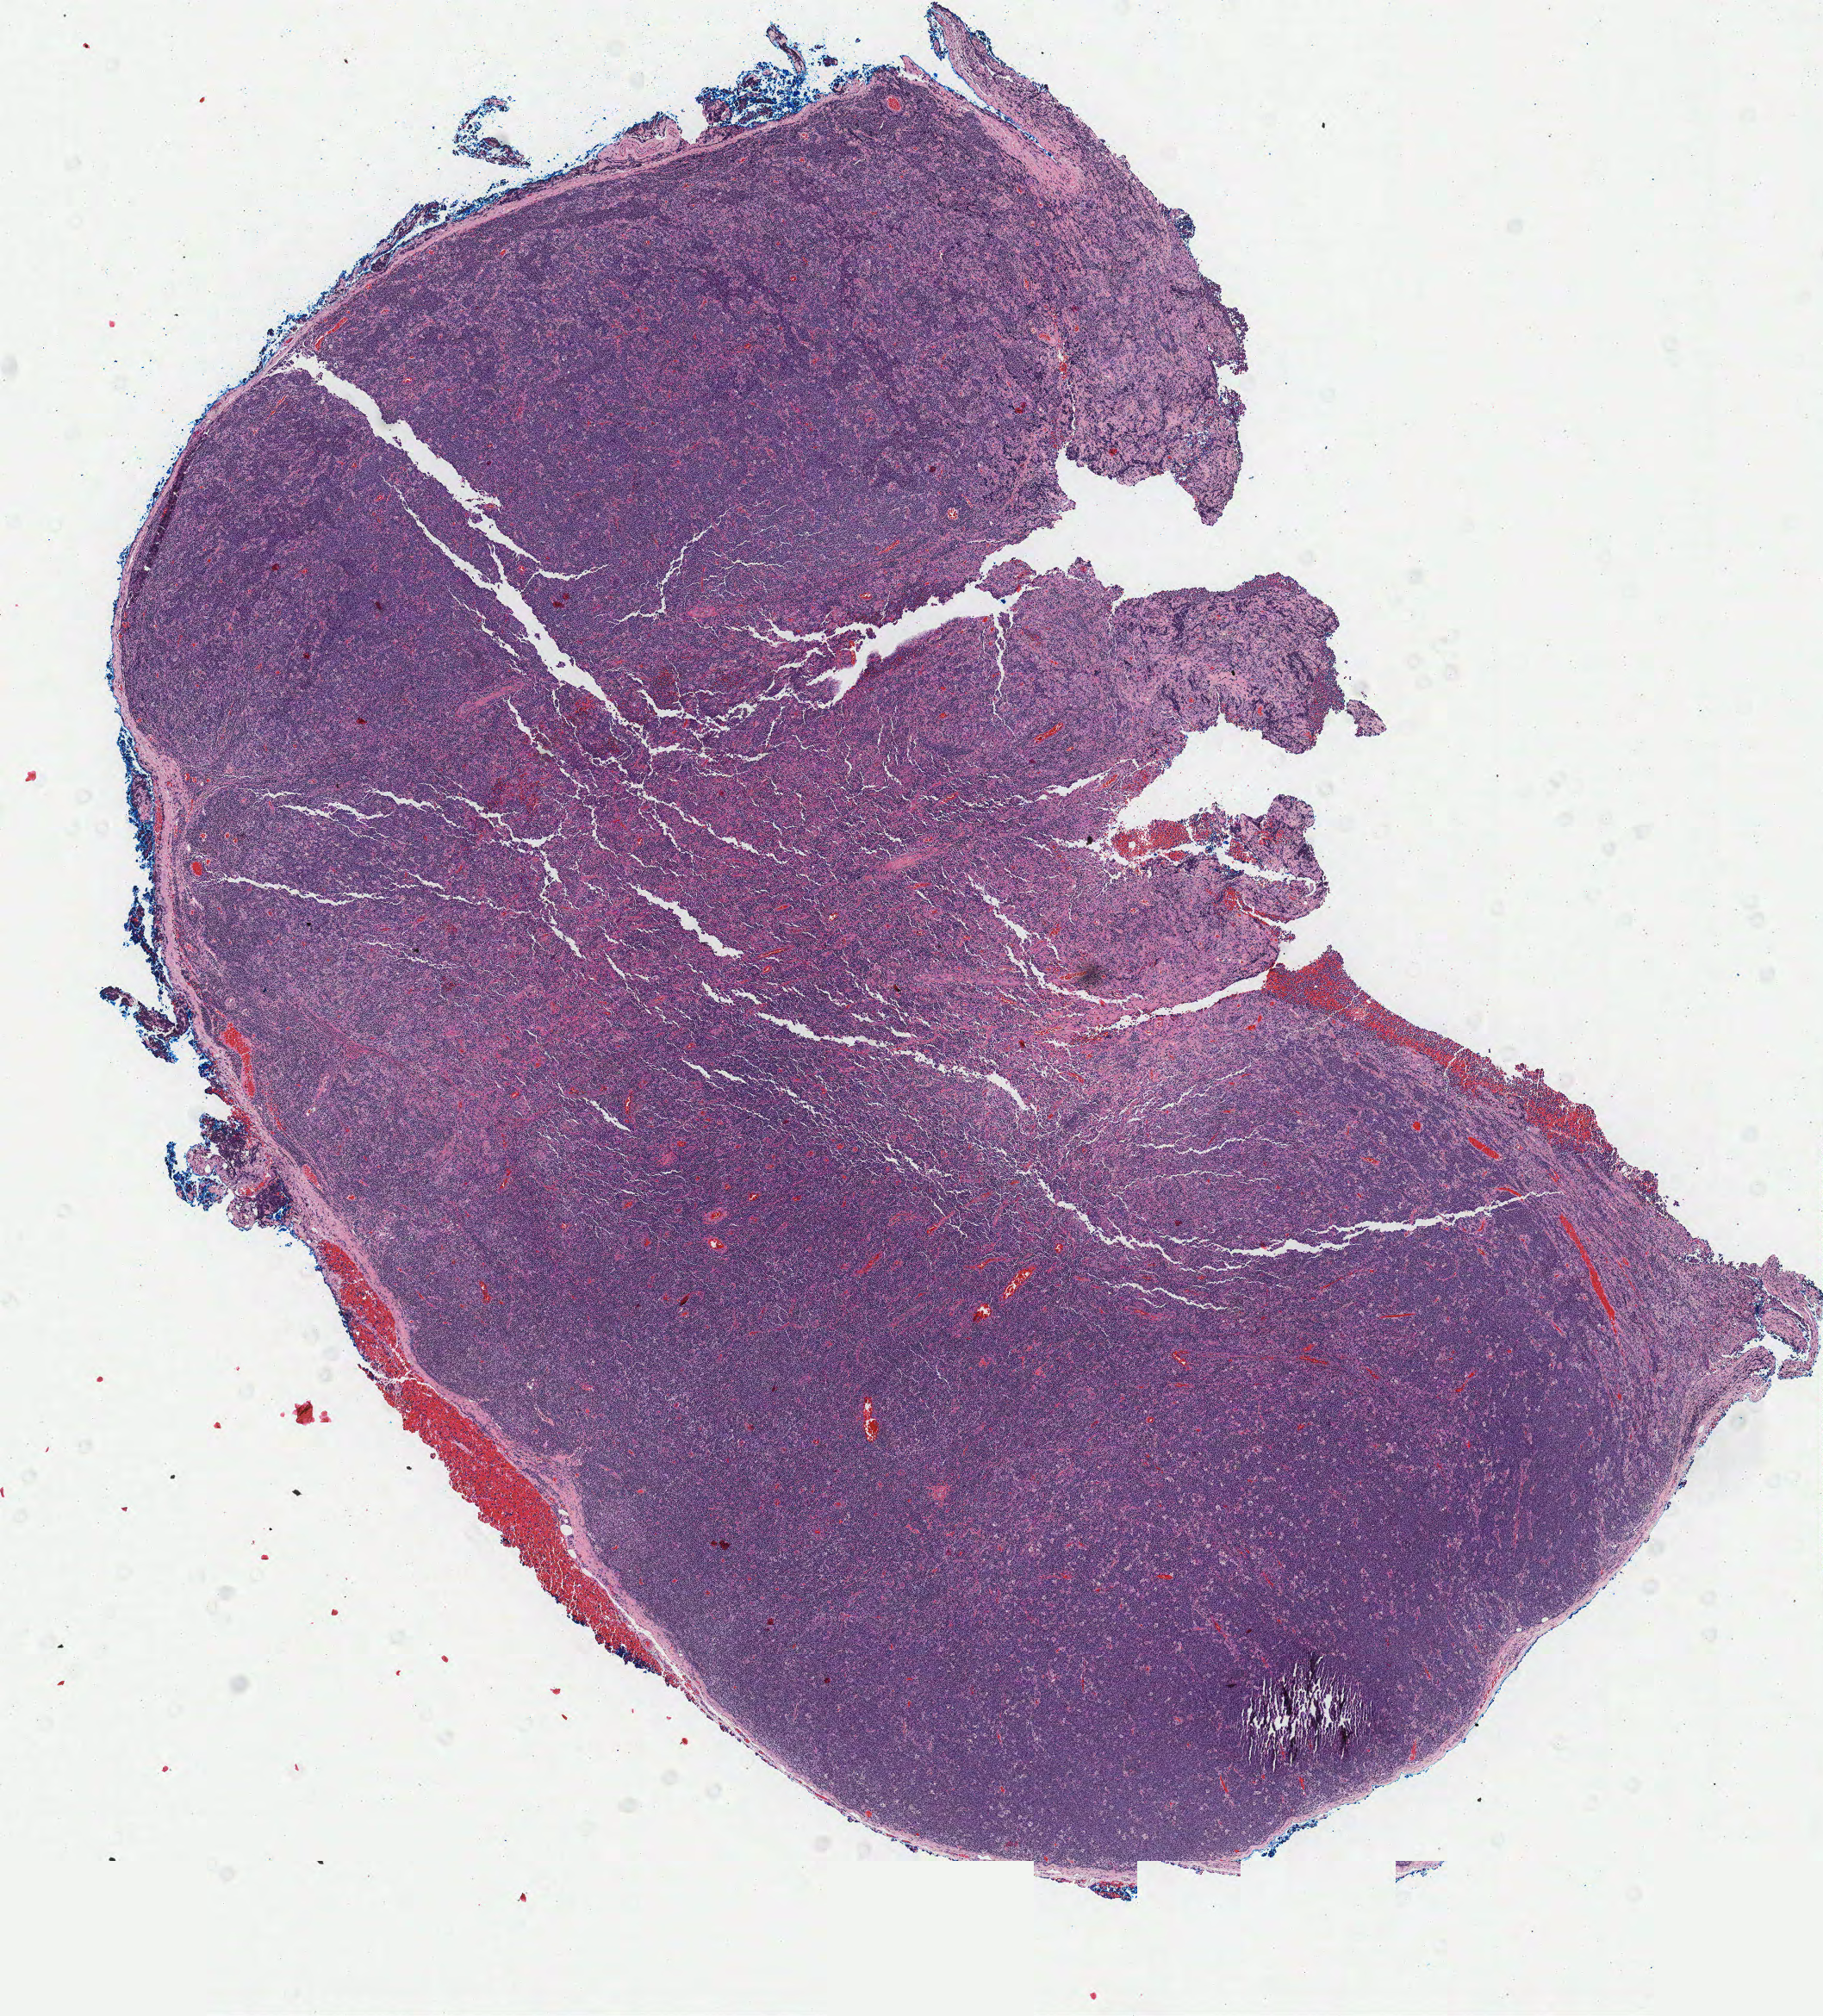
Whole-slide image, H&E stain — low-resolution overview of the scanned area, about 8.4 x 9.3 mm; formalin-fixed, paraffin-embedded (FFPE) tissue; primary tumor. Patient male; age 47 years. Slide review estimates, as recorded: tumor cells 70%, tumor nuclei 80%, stromal cells 10%, necrosis 0%, normal cells 20%. Inflammatory infiltration, as recorded: lymphocyte infiltration 80%, monocyte infiltration 10%, neutrophil infiltration 0%.
Section: top of the tissue portion. Histologic diagnosis: Burkitt lymphoma, NOS. Ann Arbor stage (patient): Stage I.